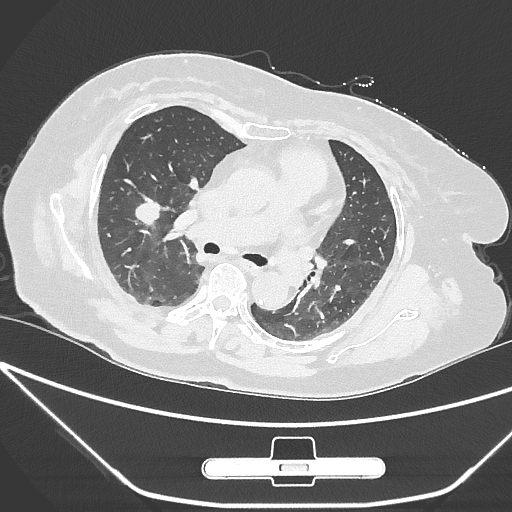
Chest CT, one axial slice; position 159 of 245 along the scan axis; reconstruction kernel IMR1,SharpPlus; 120 kVp; lung window (W 1500 / L -600 HU); 512 × 512 image matrix, field of view 365 × 365 mm. Female patient, age 65 years. From the clinical record (not read from this slice): clinical TNM (as recorded): T1c N0 M0; histopathological grade: G3.
Annotated regions visible in this slice (bounding box drawn by a radiologist):
- lung tumour (recorded histology: adenocarcinoma): bounding box <122,187,168,235> (left, top, right, bottom; pixels)